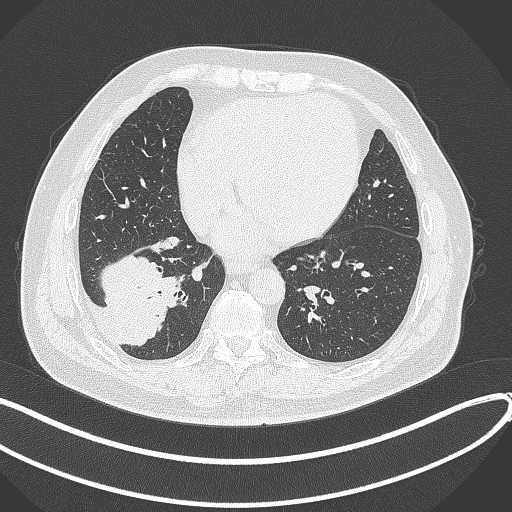
Chest CT, one axial slice. Position 123 of 360 along the scan axis. 120 kVp. Lung window (W 1500 / L -600 HU). 1 mm slice thickness. 512 × 512 image matrix, field of view 400 × 400 mm. Patient: male, 59 years.
Structures marked on this image (bounding box drawn by a radiologist):
- lung tumour (recorded histology: adenocarcinoma): bounding box (x1, y1, x2, y2) in pixels: (99, 250, 192, 345)